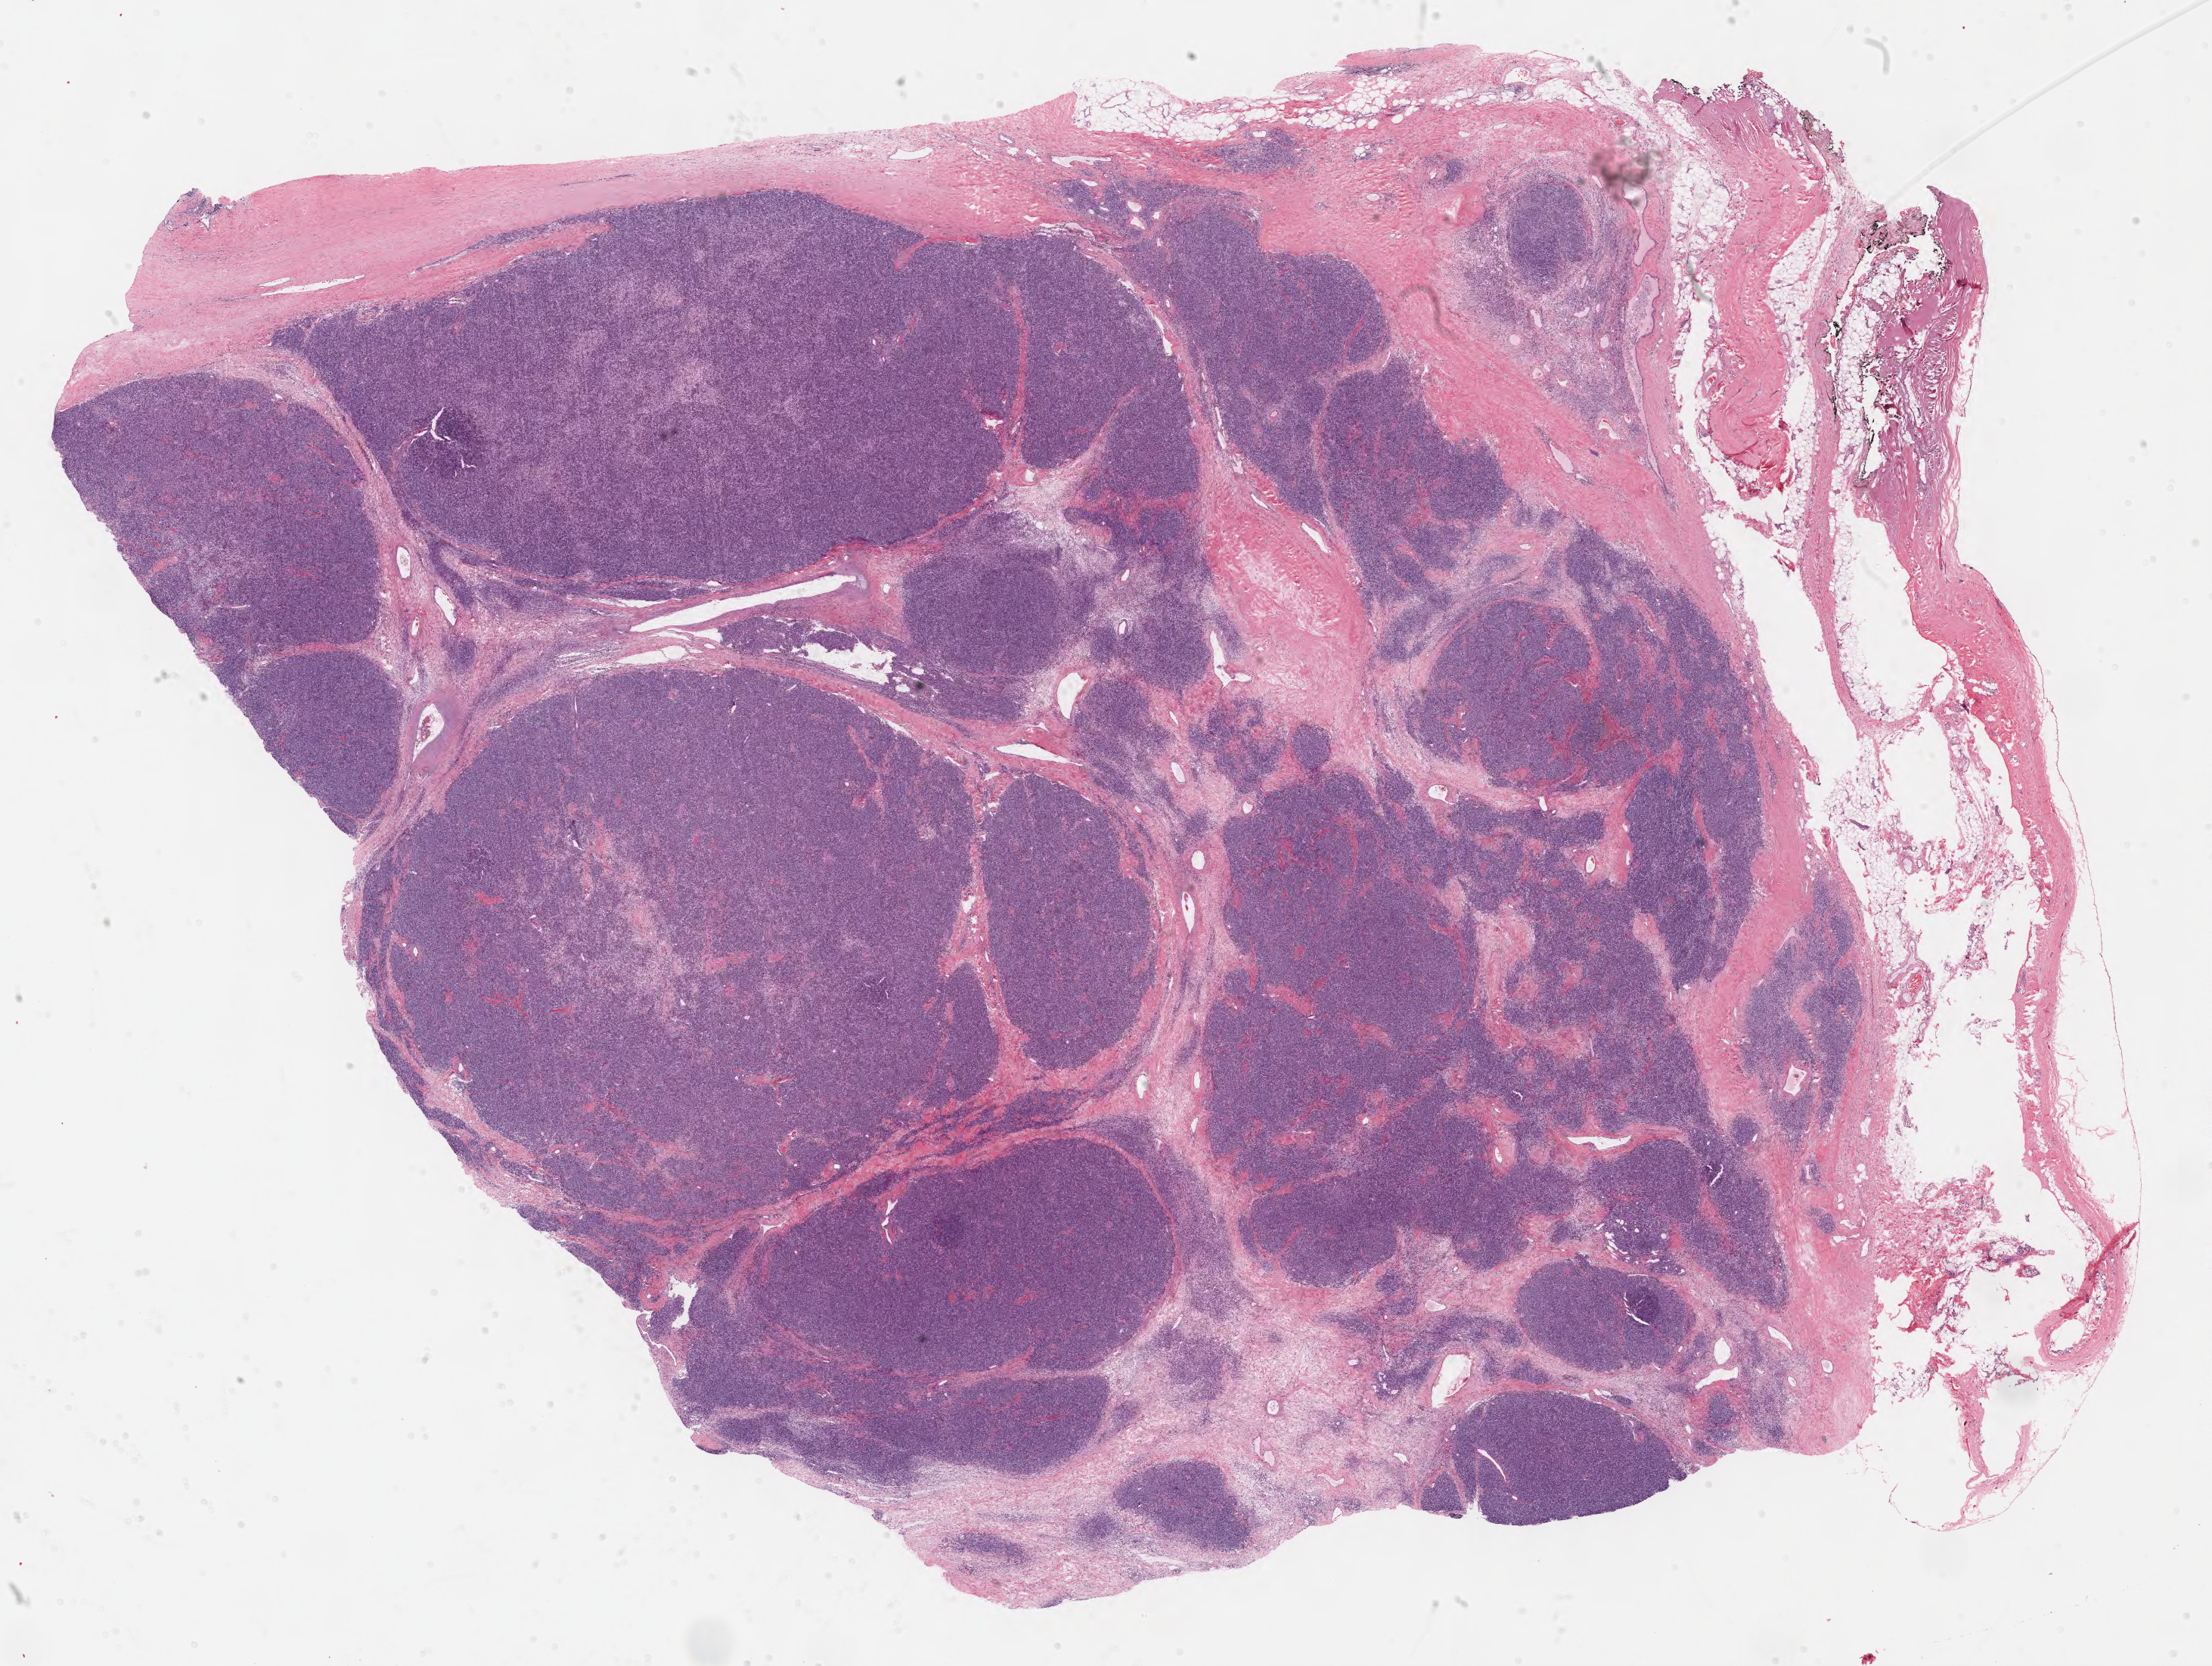
Digitized Hematoxylin and eosin (H&E) stained tissue section (whole slide) — whole scanned area (about 23.6 x 17.8 mm, slide scanned at 40x) shown as a low-resolution overview; formalin-fixed paraffin-embedded (FFPE) diagnostic section; thymus, primary tumour sample. Patient: male, age at initial diagnosis 66 years.
Pathologic diagnosis: Thymoma, type A, malignant.